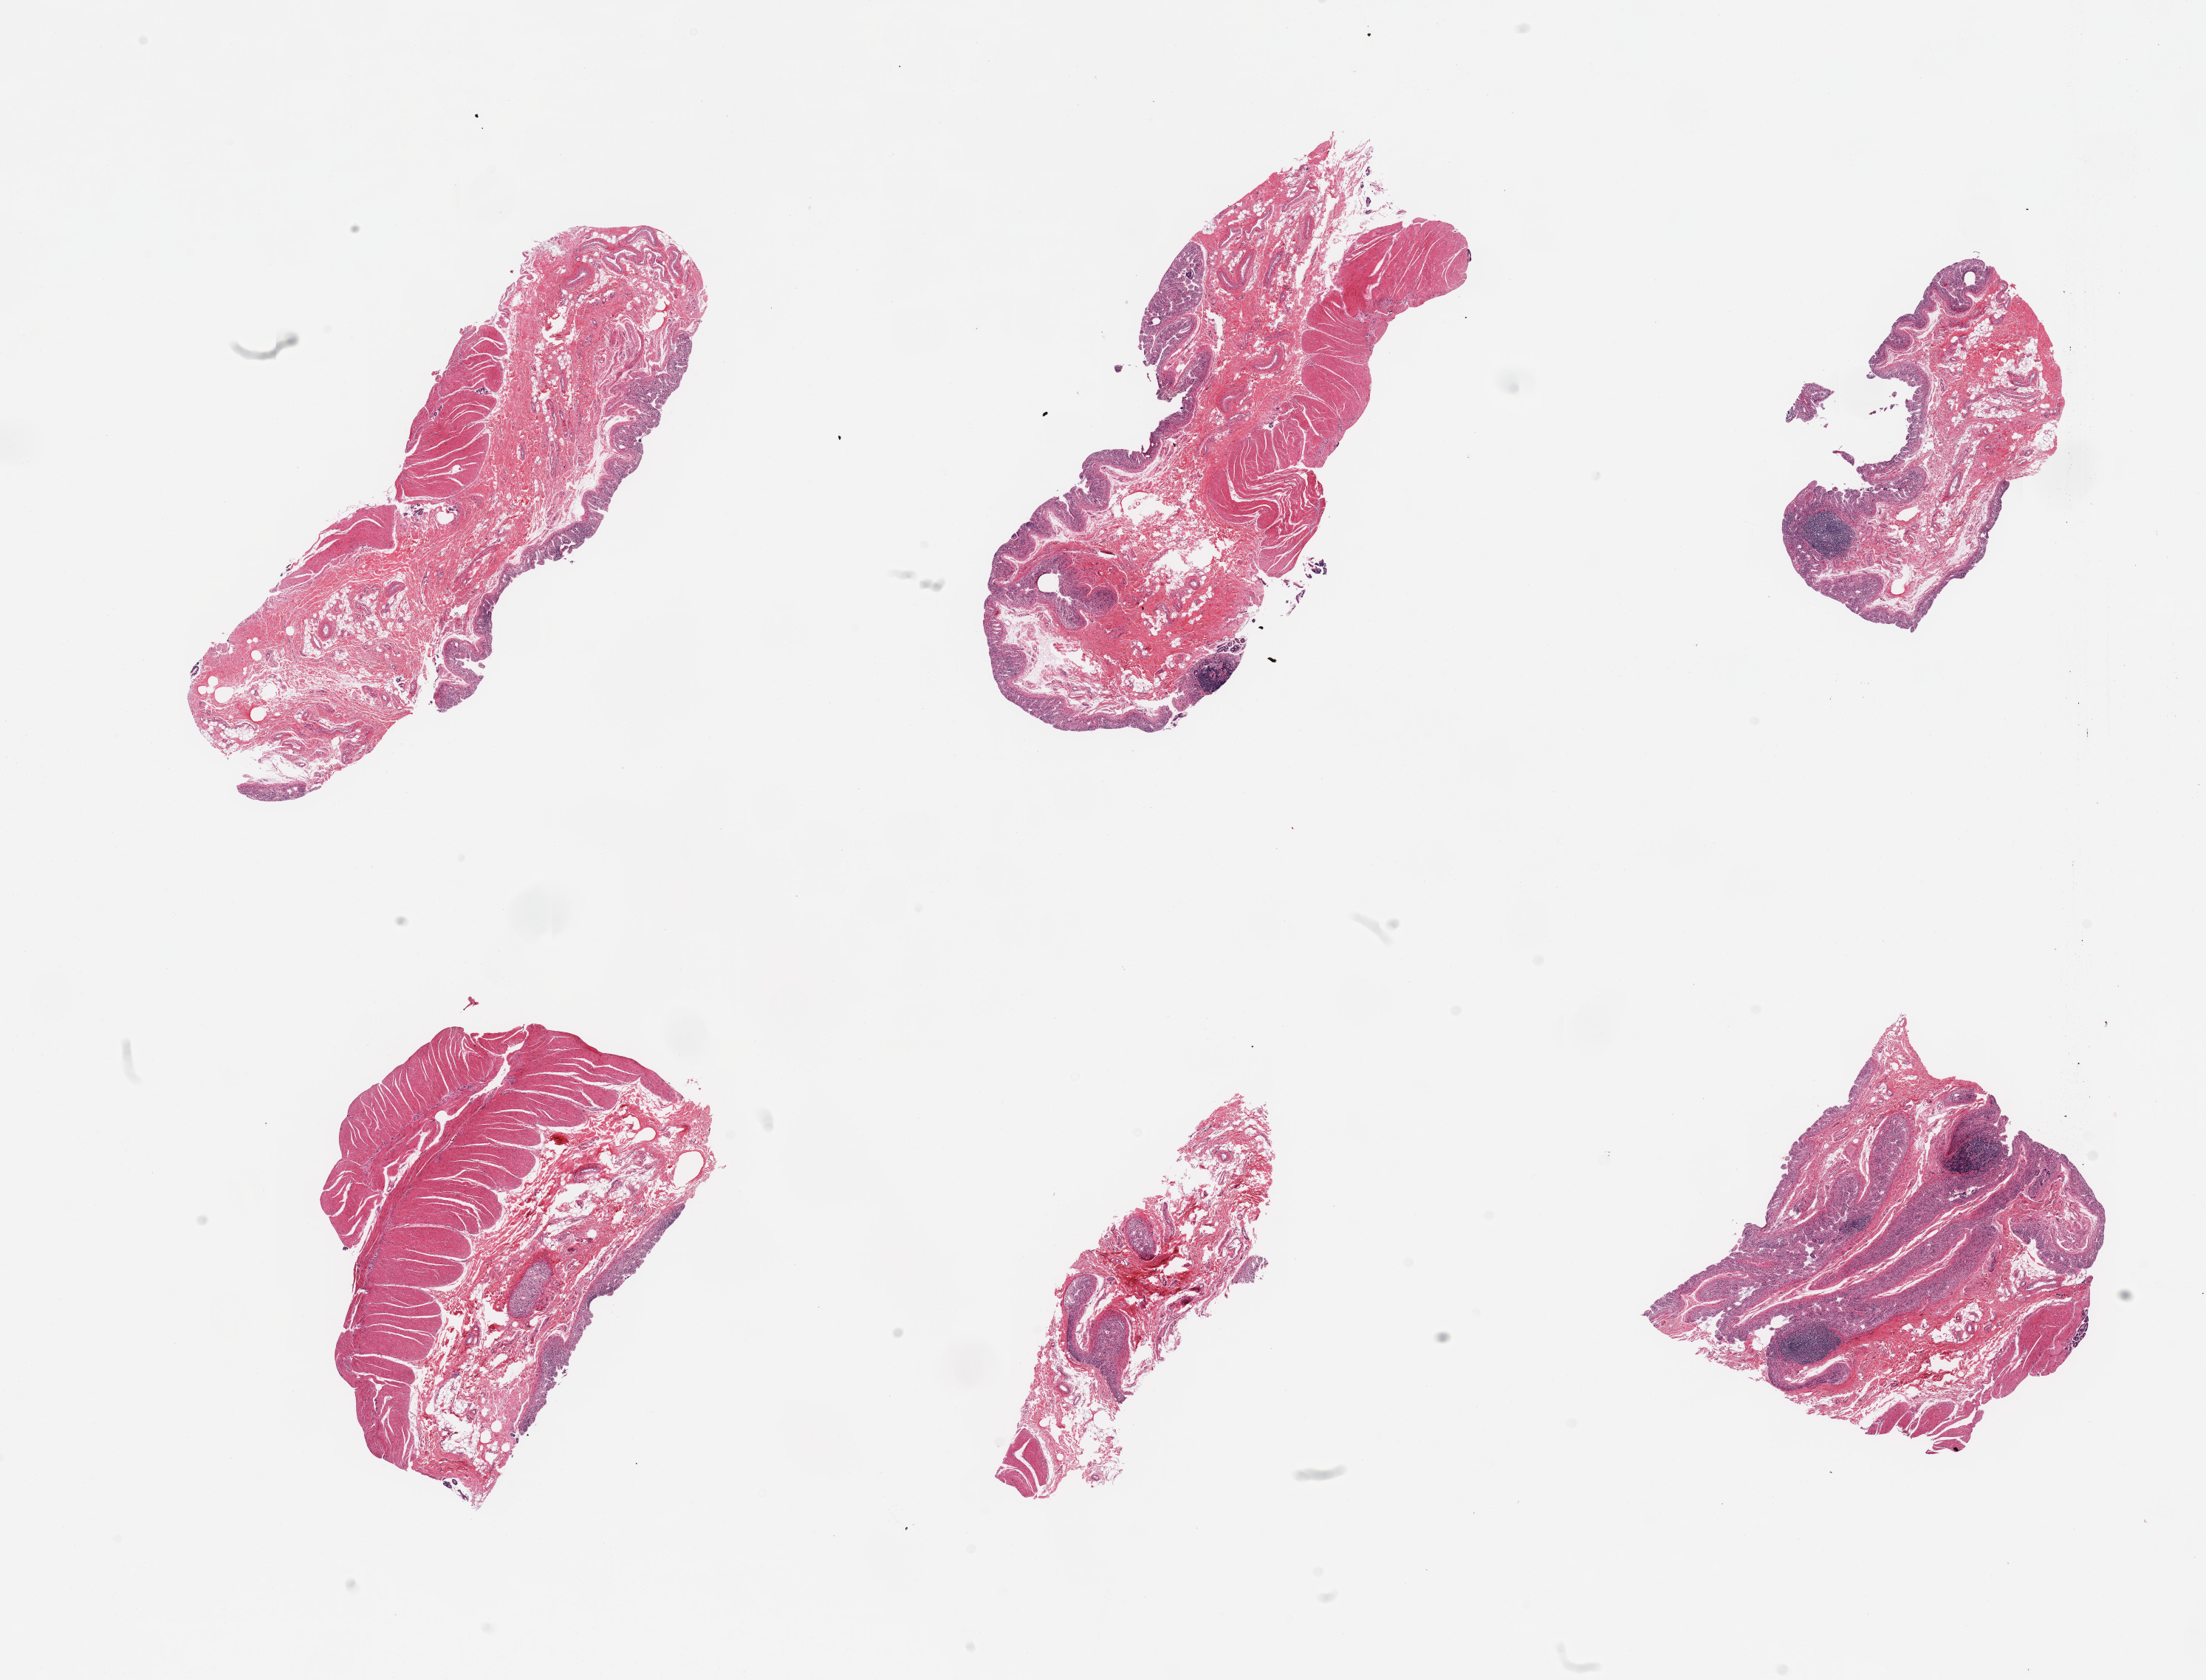
Haematoxylin and eosin whole-slide image — a low-resolution overview of the entire scanned area, about 23.6 x 18.0 mm (slide scanned at 20x). PAXgene-fixed, paraffin-embedded tissue. Section of ileum (target tissue). Donor tissue sample.
Review note (as recorded): 6 pieces, glandular mucosa completely autolyzed, target lymphoid aggregates are ~10-20% tissue.